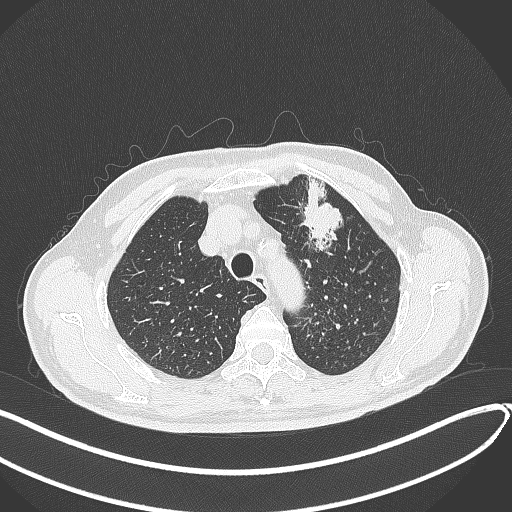
Chest CT, one axial slice. Slice 337 of 459 in the series (ordered by position). Lung window (W 1500 / L -600 HU). 1 mm slice thickness. 512 × 512 image matrix, field of view 400 × 400 mm. Male patient, age 74 years. Case-level facts recorded for this patient, not image findings: clinical TNM (as recorded): T2b N0 M1c.
Annotated regions visible in this slice (rectangle marked by the reading radiologist):
- lung tumour (recorded histology: adenocarcinoma): bounding box <298,173,349,252> (left, top, right, bottom; pixels)